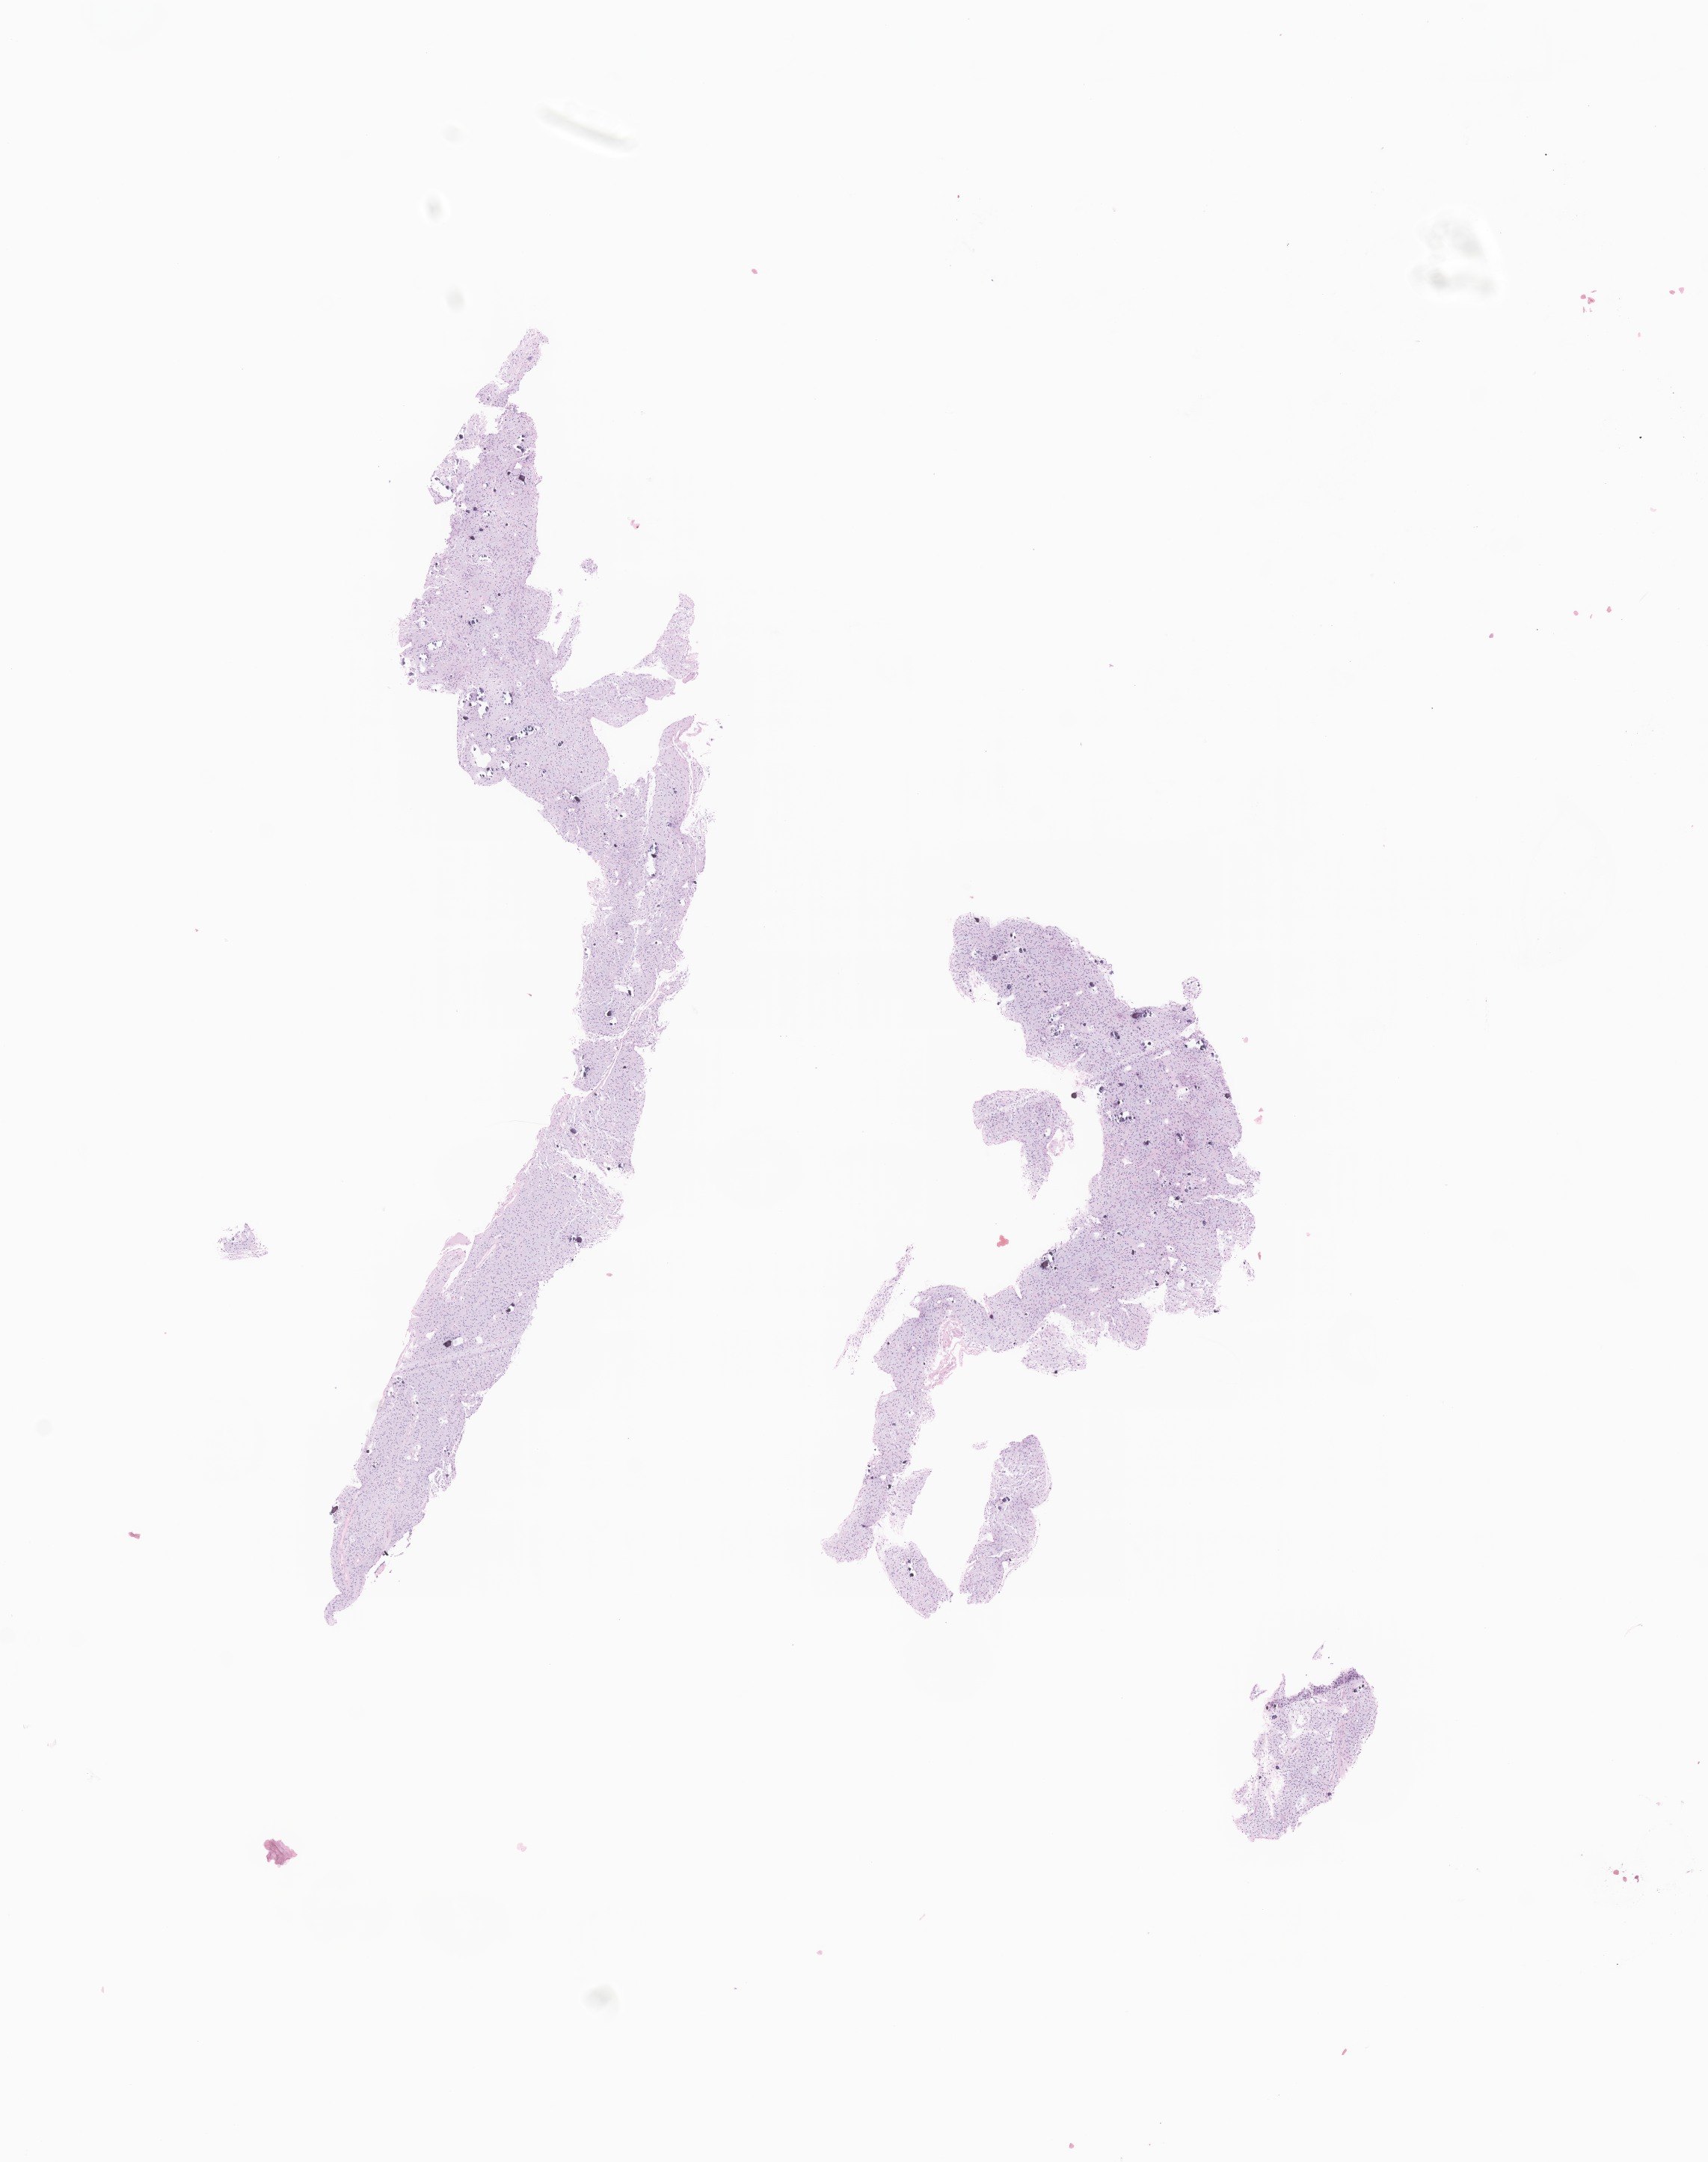
H&E whole-slide image of tumor tissue from the brain, shown as a low-resolution overview of the whole scanned area (about 9.6 x 12.2 mm), formalin-fixed paraffin-embedded section. Male patient, age 103 months (8 years 7 months).
Recorded diagnosis: Astrocytoma, NOS.